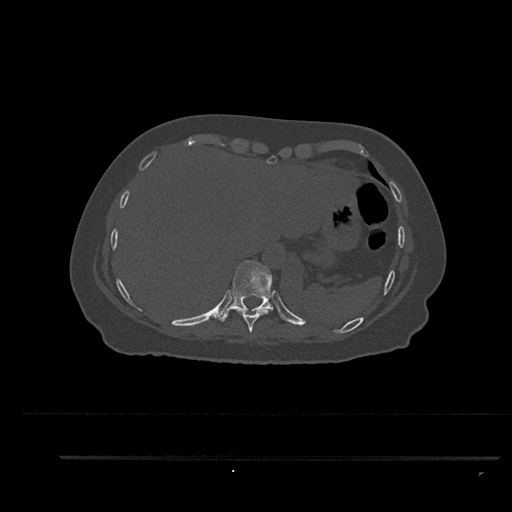
CT including the spine, one axial slice; position 389 of 797 along the scan axis; reconstruction kernel Br40s/3; 120 kVp; bone window (W 1800 / L 400 HU); 0.5 mm slice thickness; 512 × 512 image matrix. Patient: female, 44 years. From the clinical record (not read from this slice): primary cancer: renal.
Outlined on this slice (semi-automatically segmented with operator editing):
- T10 vertebra: bounding box (x1, y1, x2, y2) in pixels: (216, 260, 274, 322)
- T9 vertebra: (236, 309, 273, 333)